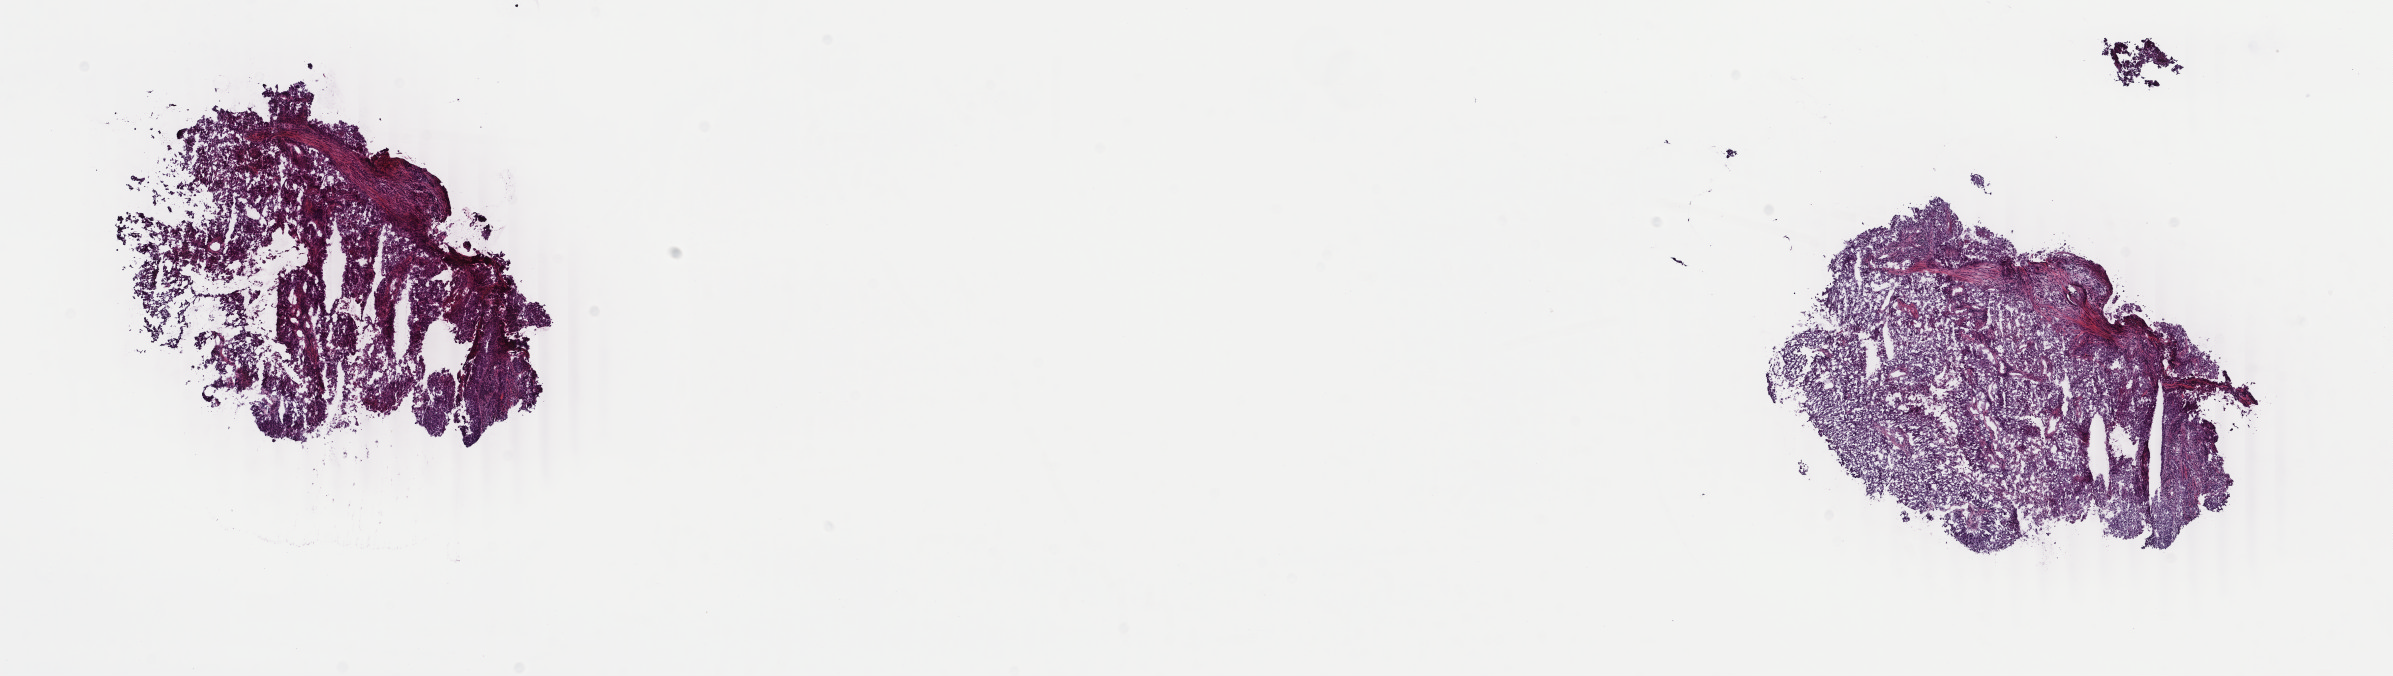
Whole-slide histology image, H&E, whole scanned area (about 19.0 x 5.4 mm, from a 40x scan) shown as a low-resolution overview, frozen section, lung, primary tumour sample. Male, age 76 years at initial diagnosis. Composition of this section per pathologist review: tumour cells 100%, tumour nuclei 75%, normal cells 0%, stromal cells 0%, necrosis 0%. Inflammatory infiltration, as recorded: lymphocyte infiltration 0%, monocyte infiltration 0%, neutrophil infiltration 0%.
AJCC pathologic stage: IB (7th edition). Histologic diagnosis: Squamous cell carcinoma, NOS (upper lobe, lung). Laterality: right.